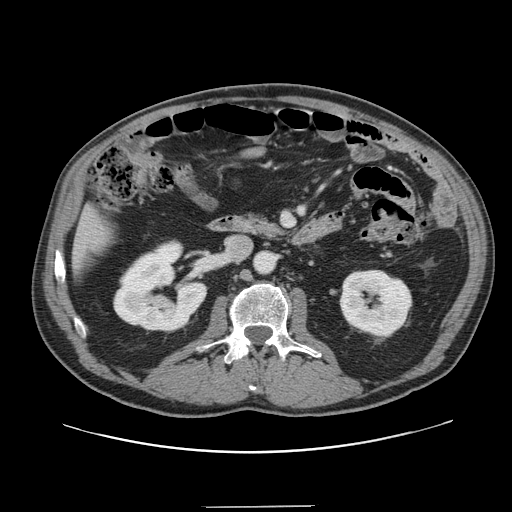
Contrast-enhanced abdominal CT, one axial slice. Position 54 of 139 along the scan axis. 120 kVp. Intravenous contrast given. Soft-tissue window (W 400 / L 40 HU). 512 × 512 image matrix. Male patient, age 64 years. From the clinical record (not read from this slice): diagnosis: colorectal cancer liver metastases, imaged before liver resection; multiple liver metastases: yes; largest metastasis: 3.5 cm.
Annotated regions visible in this slice (expert manual segmentation):
- liver: bounding box [x1, y1, x2, y2] px = [75, 211, 111, 270]
- planned liver remnant (the part of the liver to remain after resection): [74, 211, 110, 272]